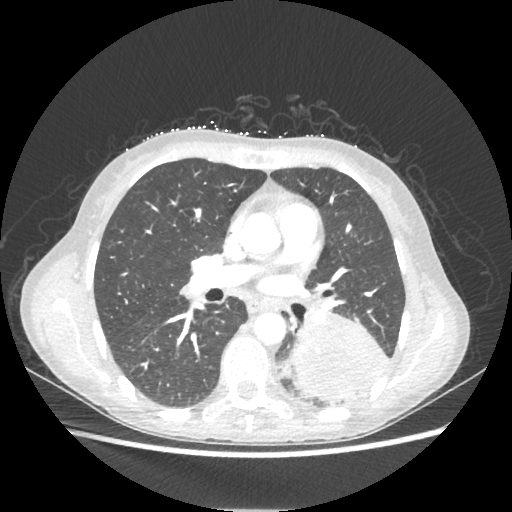
Chest CT, one axial slice; position 119 of 221 along the scan axis; reconstruction kernel STANDARD; lung window (W 1500 / L -600 HU); 1.25 mm slice thickness; 512 × 512 image matrix, field of view 360 × 360 mm. Patient: female, 53 years. From the clinical record (not read from this slice): clinical TNM (as recorded): T3 N0 M0.
Annotated regions visible in this slice (rectangle marked by the reading radiologist):
- lung tumour (recorded histology: adenocarcinoma): bounding box (x1, y1, x2, y2) in pixels: (290, 304, 388, 406)